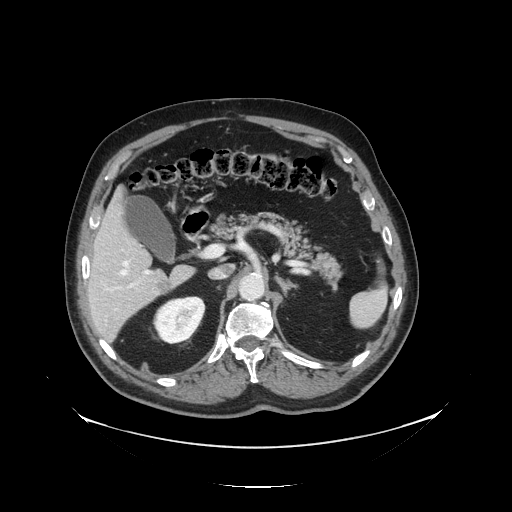
Contrast-enhanced abdominal CT, one axial slice; position 77 of 138 along the scan axis; soft-tissue window (W 400 / L 40 HU); 2.5 mm slice thickness; 512 × 512 image matrix. Male patient, age 77 years. From the clinical record (not read from this slice): diagnosis: colorectal cancer liver metastases, imaged before liver resection; multiple liver metastases: no; largest metastasis: 1.5 cm; disease in both lobes: no.
Annotated regions visible in this slice (expert manual segmentation):
- hepatic veins: bounding box (x1, y1, x2, y2) in pixels: (120, 261, 128, 276)
- liver: (86, 192, 194, 341)
- planned liver remnant (the part of the liver to remain after resection): (87, 194, 154, 287)
- portal vein (with intrahepatic branches): (115, 255, 204, 310)
- liver metastasis: (158, 282, 172, 296)